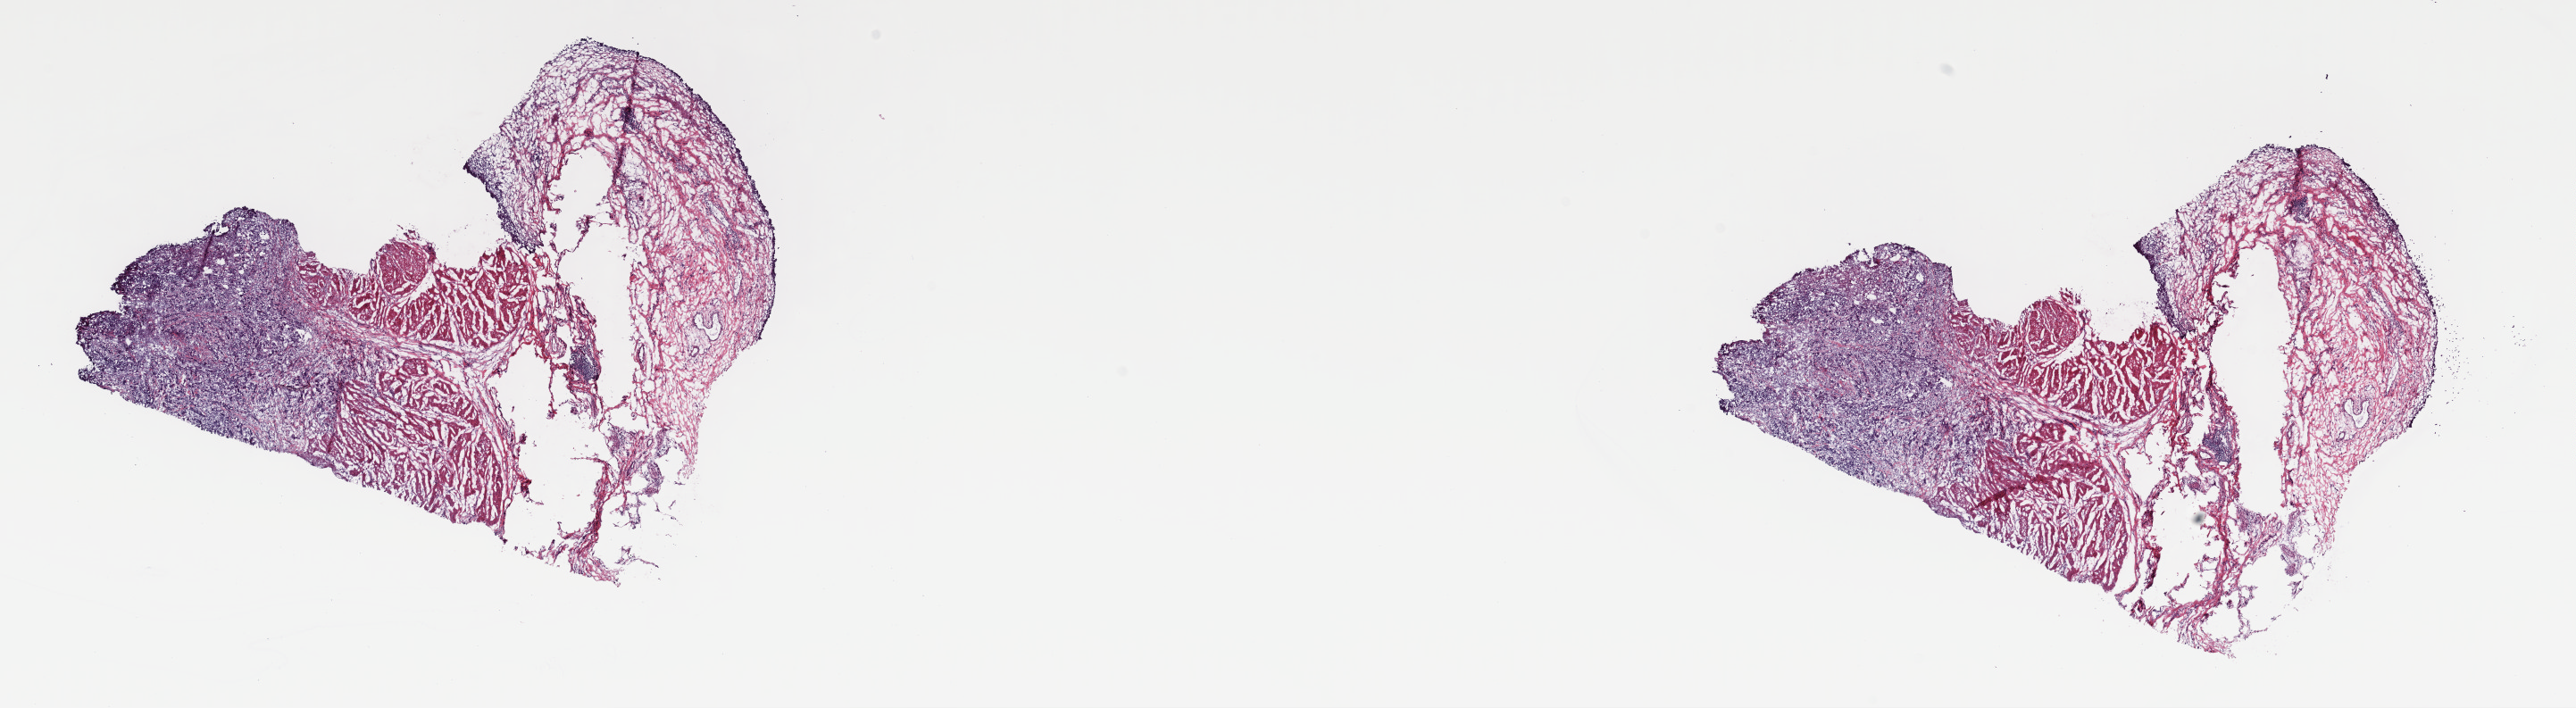
Whole-slide histology image, H&E — low-resolution overview of the scanned area, about 22.8 x 6.3 mm (slide scanned at 40x), frozen section, bladder, primary tumour sample. Patient: male, age at initial diagnosis 76 years. Histologic grade: high grade. Pathologist review of this section (percent, as recorded): tumour cells 19%, tumour nuclei 75%, normal cells 3%, stromal cells 75%, necrosis 3%. Infiltration values recorded for this section: lymphocyte infiltration 5%, monocyte infiltration 2%, neutrophil infiltration 3%.
AJCC pathologic stage: IV (7th edition). Lymph nodes positive (case pathology): 2 of 14 examined. Histologic diagnosis: Transitional cell carcinoma.